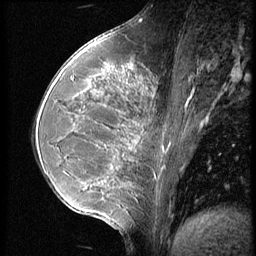
Breast MRI (dynamic contrast-enhanced), one sagittal slice; position 24 of 56 along the scan axis; 3 images stored at this slice position (order not interpretable as contrast timing); 1.5 T; TE 4.2 ms, TR 9 ms; 2.5 mm slice thickness; 256 × 256 image matrix, field of view 180 × 180 mm. Female patient, age 35 years. Case-level facts recorded for this patient, not image findings: setting: breast cancer imaged before/during neoadjuvant chemotherapy; receptor status: HR-positive, HER2-negative.
Annotated regions visible in this slice (semi-automatically segmented with operator editing):
- analysis volume of interest (the breast-tissue region the enhancement analysis was run in; not a lesion): bounding box (x1, y1, x2, y2) in pixels: (63, 60, 176, 218)
- tumour enhancement mask (voxels above the 140 % enhancement threshold inside the analysis volume of interest): (102, 67, 139, 184)